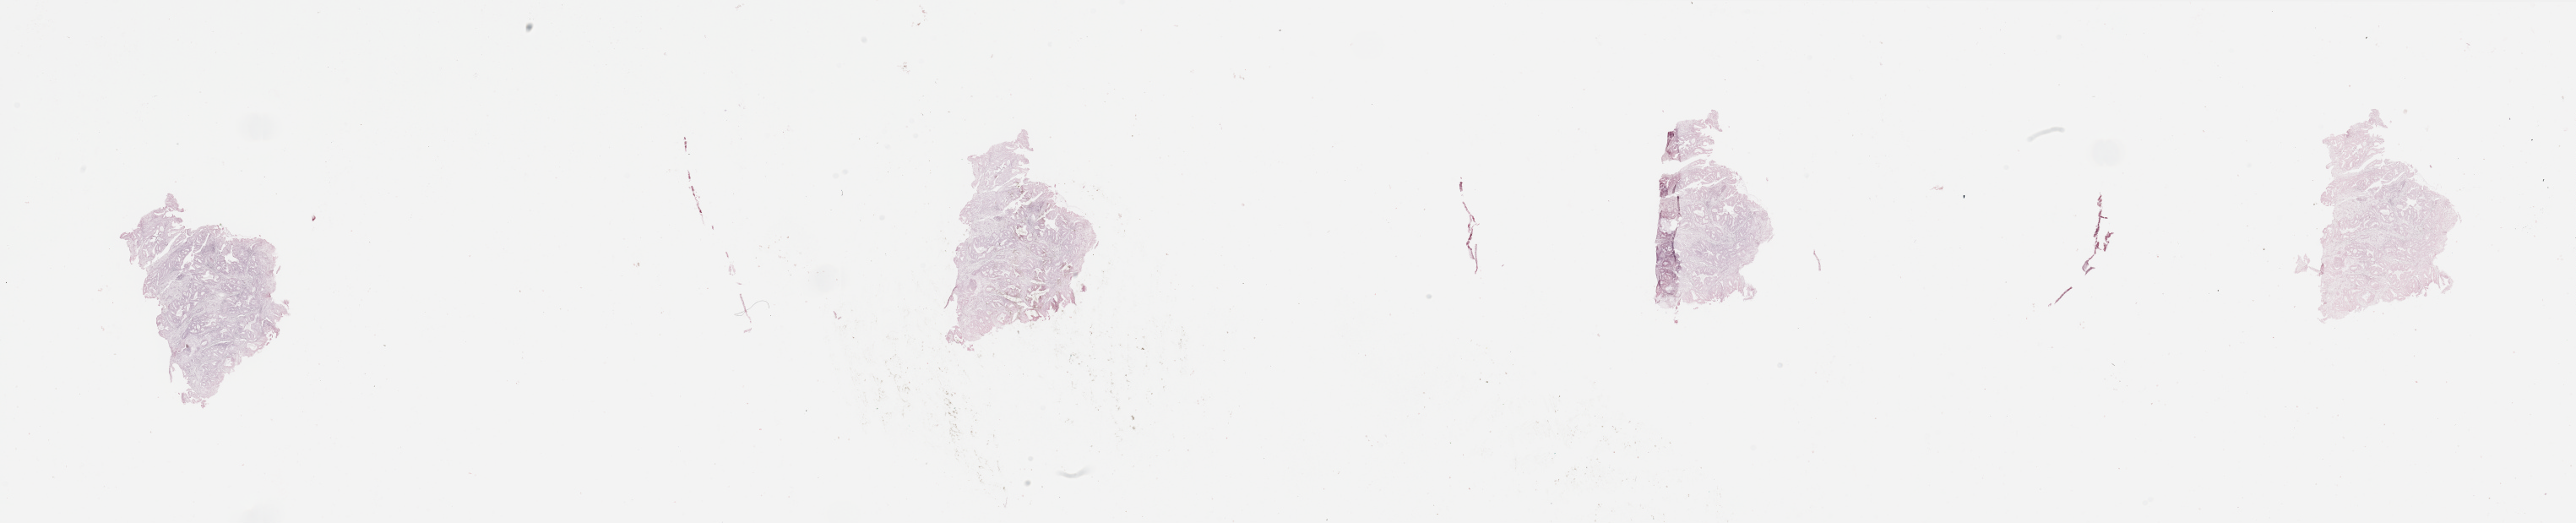
Digitized Hematoxylin and eosin (H&E) stained tissue section (whole slide) — low-resolution overview of the scanned area, about 48.2 x 9.8 mm. Tumour tissue sample, sampled site: uterus. 75-year-old female patient. Histologic grade: G1 (well differentiated). Slide review estimates, as recorded: tumour nuclei 80%, necrosis 0%.
• histologic diagnosis: Endometrioid adenocarcinoma, NOS
• AJCC pathologic stage: I